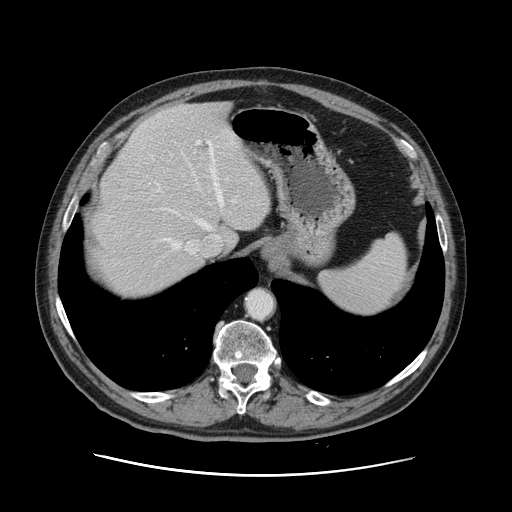
Contrast-enhanced abdominal CT, one axial slice. Position 102 of 141 along the scan axis. Intravenous contrast given. Soft-tissue window (W 400 / L 40 HU). 2.5 mm slice thickness. 512 × 512 image matrix, field of view 395 × 395 mm. Male patient, age 72 years. Case-level facts recorded for this patient, not image findings: diagnosis: colorectal cancer liver metastases, imaged before liver resection; multiple liver metastases: yes; largest metastasis: 5.4 cm.
Outlined on this slice (outlined manually by an expert reader):
- hepatic veins: bounding box [x1, y1, x2, y2] px = [157, 141, 223, 254]
- liver: [93, 102, 272, 299]
- planned liver remnant (the part of the liver to remain after resection): [101, 102, 272, 299]
- portal vein (with intrahepatic branches): [193, 141, 236, 251]